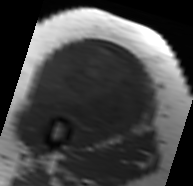
MRI of an extremity soft-tissue mass, one axial slice. Slice 38 of 91 in the series (ordered by position). MR volume resampled by the dataset authors to the PET/CT grid (not the native acquisition matrix). 193 × 186 image matrix, field of view 188 × 182 mm. Female patient. From the clinical record (not read from this slice): histological type: malignant solitary fibrous tumor; grade: intermediate; site of the primary tumour: right thigh.
Structures marked on this image (expert contour drawn on MRI and transferred to this co-registered scan by the dataset authors):
- gross tumour volume including surrounding oedema: box from (x=26, y=42) to (x=153, y=138) px
- gross tumour volume (mass): (x=33, y=42)–(x=148, y=134)